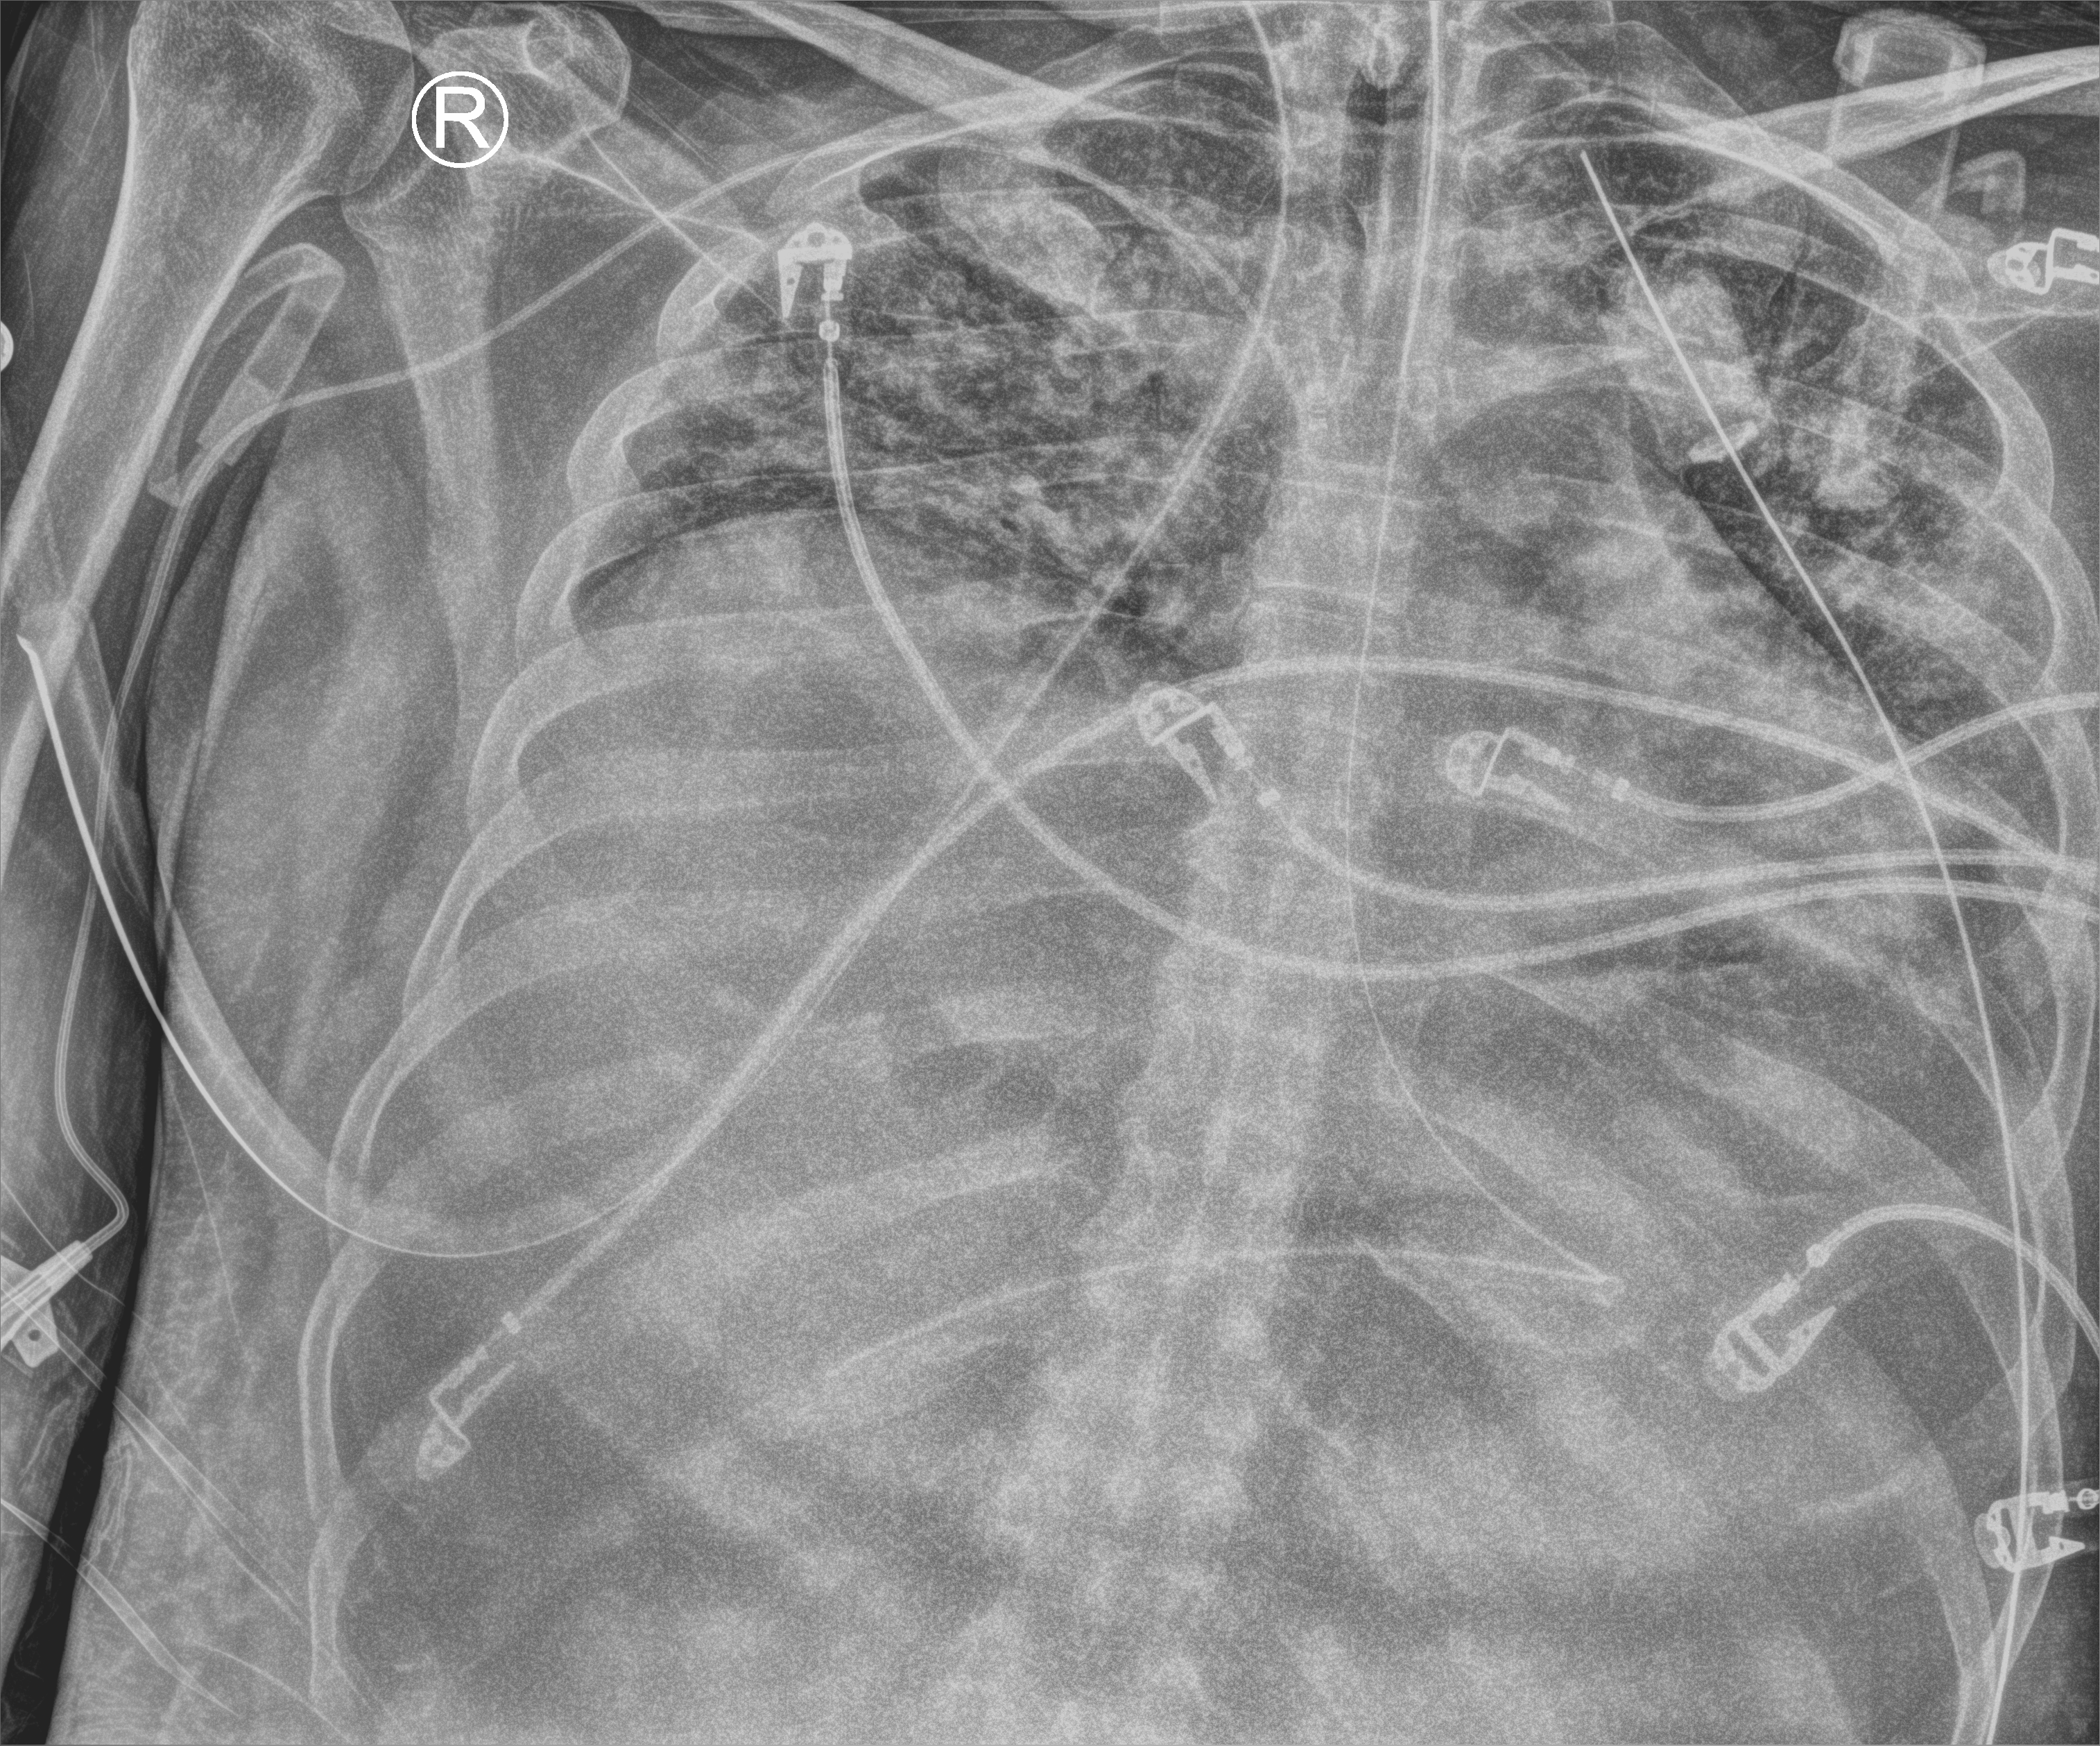
Portable chest radiograph, anteroposterior (AP) projection. Male patient hospitalised with COVID-19, age 18–59 years.
From the hospital-stay record, not from the radiograph (when in the stay this image was taken is not recorded): length of hospital stay: 48 days; smoking status (admission record): never.